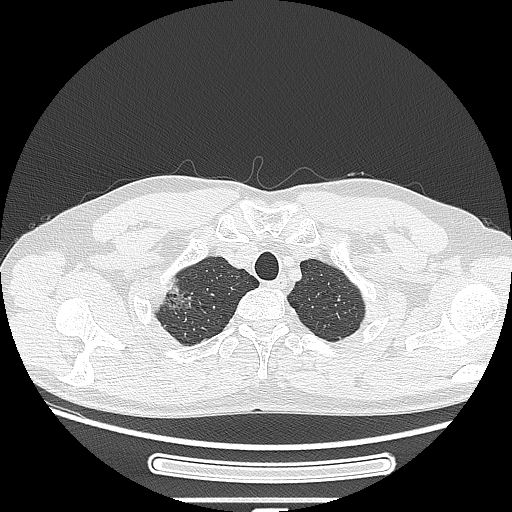
Chest CT, one axial slice; position 236 of 269 along the scan axis; reconstruction kernel LUNG; 120 kVp; lung window (W 1500 / L -600 HU); 1.25 mm slice thickness; 512 × 512 image matrix, field of view 382 × 382 mm. Patient: male, 53 years. From the clinical record (not read from this slice): clinical TNM (as recorded): T1c N0 M0.
Structures marked on this image (rectangle marked by the reading radiologist):
- lung tumour (recorded histology: adenocarcinoma): bounding box (x1, y1, x2, y2) in pixels: (151, 267, 193, 322)